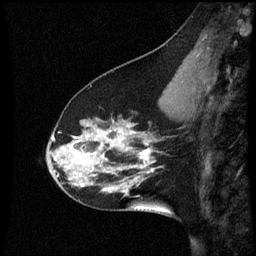
Breast MRI (dynamic contrast-enhanced), one sagittal slice; position 19 of 60 along the scan axis; dynamic contrast-enhanced series, image 2 of 3 at this slice position (ordered by acquisition); 1.5 T; TE 4.2 ms, TR 8.9 ms; 2 mm slice thickness; 256 × 256 image matrix, field of view 200 × 200 mm. Patient: female, 45 years. Case-level facts recorded for this patient, not image findings: setting: breast cancer imaged before/during neoadjuvant chemotherapy; receptor status: HR-positive, HER2-negative.
Outlined on this slice (semi-automatic segmentation, software-assisted and operator-edited):
- analysis volume of interest (the breast-tissue region the enhancement analysis was run in; not a lesion): bounding box <46,94,171,205> (left, top, right, bottom; pixels)
- tumour enhancement mask (voxels above the 70 % enhancement threshold inside the analysis volume of interest): <72,132,155,191>